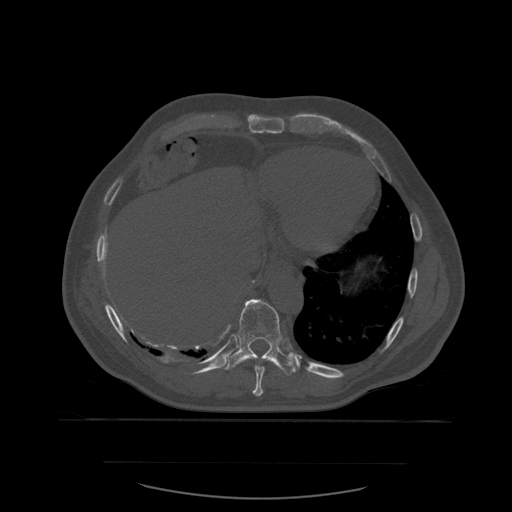
CT including the spine, one axial slice; slice 325 of 590 in the series (ordered by position); bone window (W 1800 / L 400 HU); 1.25 mm slice thickness; 512 × 512 image matrix, field of view 479 × 479 mm. Patient age 71 years. Case-level facts recorded for this patient, not image findings: primary cancer: lung; vertebrae with lytic lesions (as recorded): T1, T2, L5, S1.
Annotated regions visible in this slice (semi-automatic segmentation, software-assisted and operator-edited):
- T10 vertebra: bounding box <226,299,298,376> (left, top, right, bottom; pixels)
- T9 vertebra: <253,358,265,397>